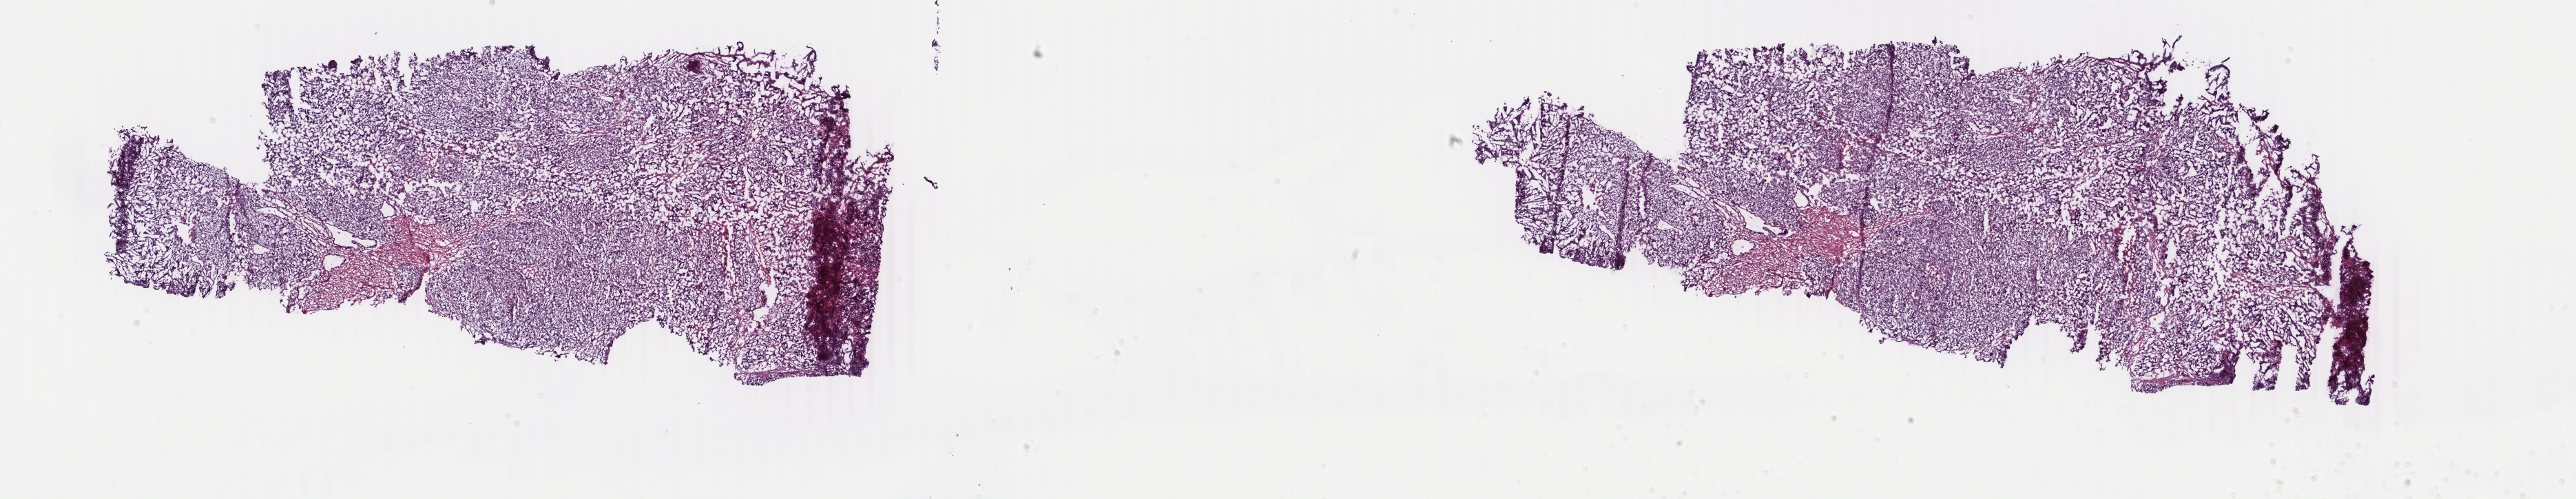
Digitized H&E tissue section (whole slide), whole scanned area (about 29.7 x 5.8 mm) shown as a low-resolution overview; frozen section from the bottom of the tissue portion; uterus, primary tumour sample. Female patient; age at initial diagnosis 80 years. Histologic grade: G2 (moderately differentiated). Pathologist review of this section (percent, as recorded): tumour cells 75%, tumour nuclei 80%, normal cells 13%, stromal cells 2%, necrosis 10%. Inflammatory infiltration, as recorded: lymphocyte infiltration 0%, monocyte infiltration 0%, neutrophil infiltration 1%.
Lymph nodes positive (case pathology): 0 of 7 examined. Diagnosis: Endometrioid adenocarcinoma, NOS (endometrium). FIGO stage: IB.